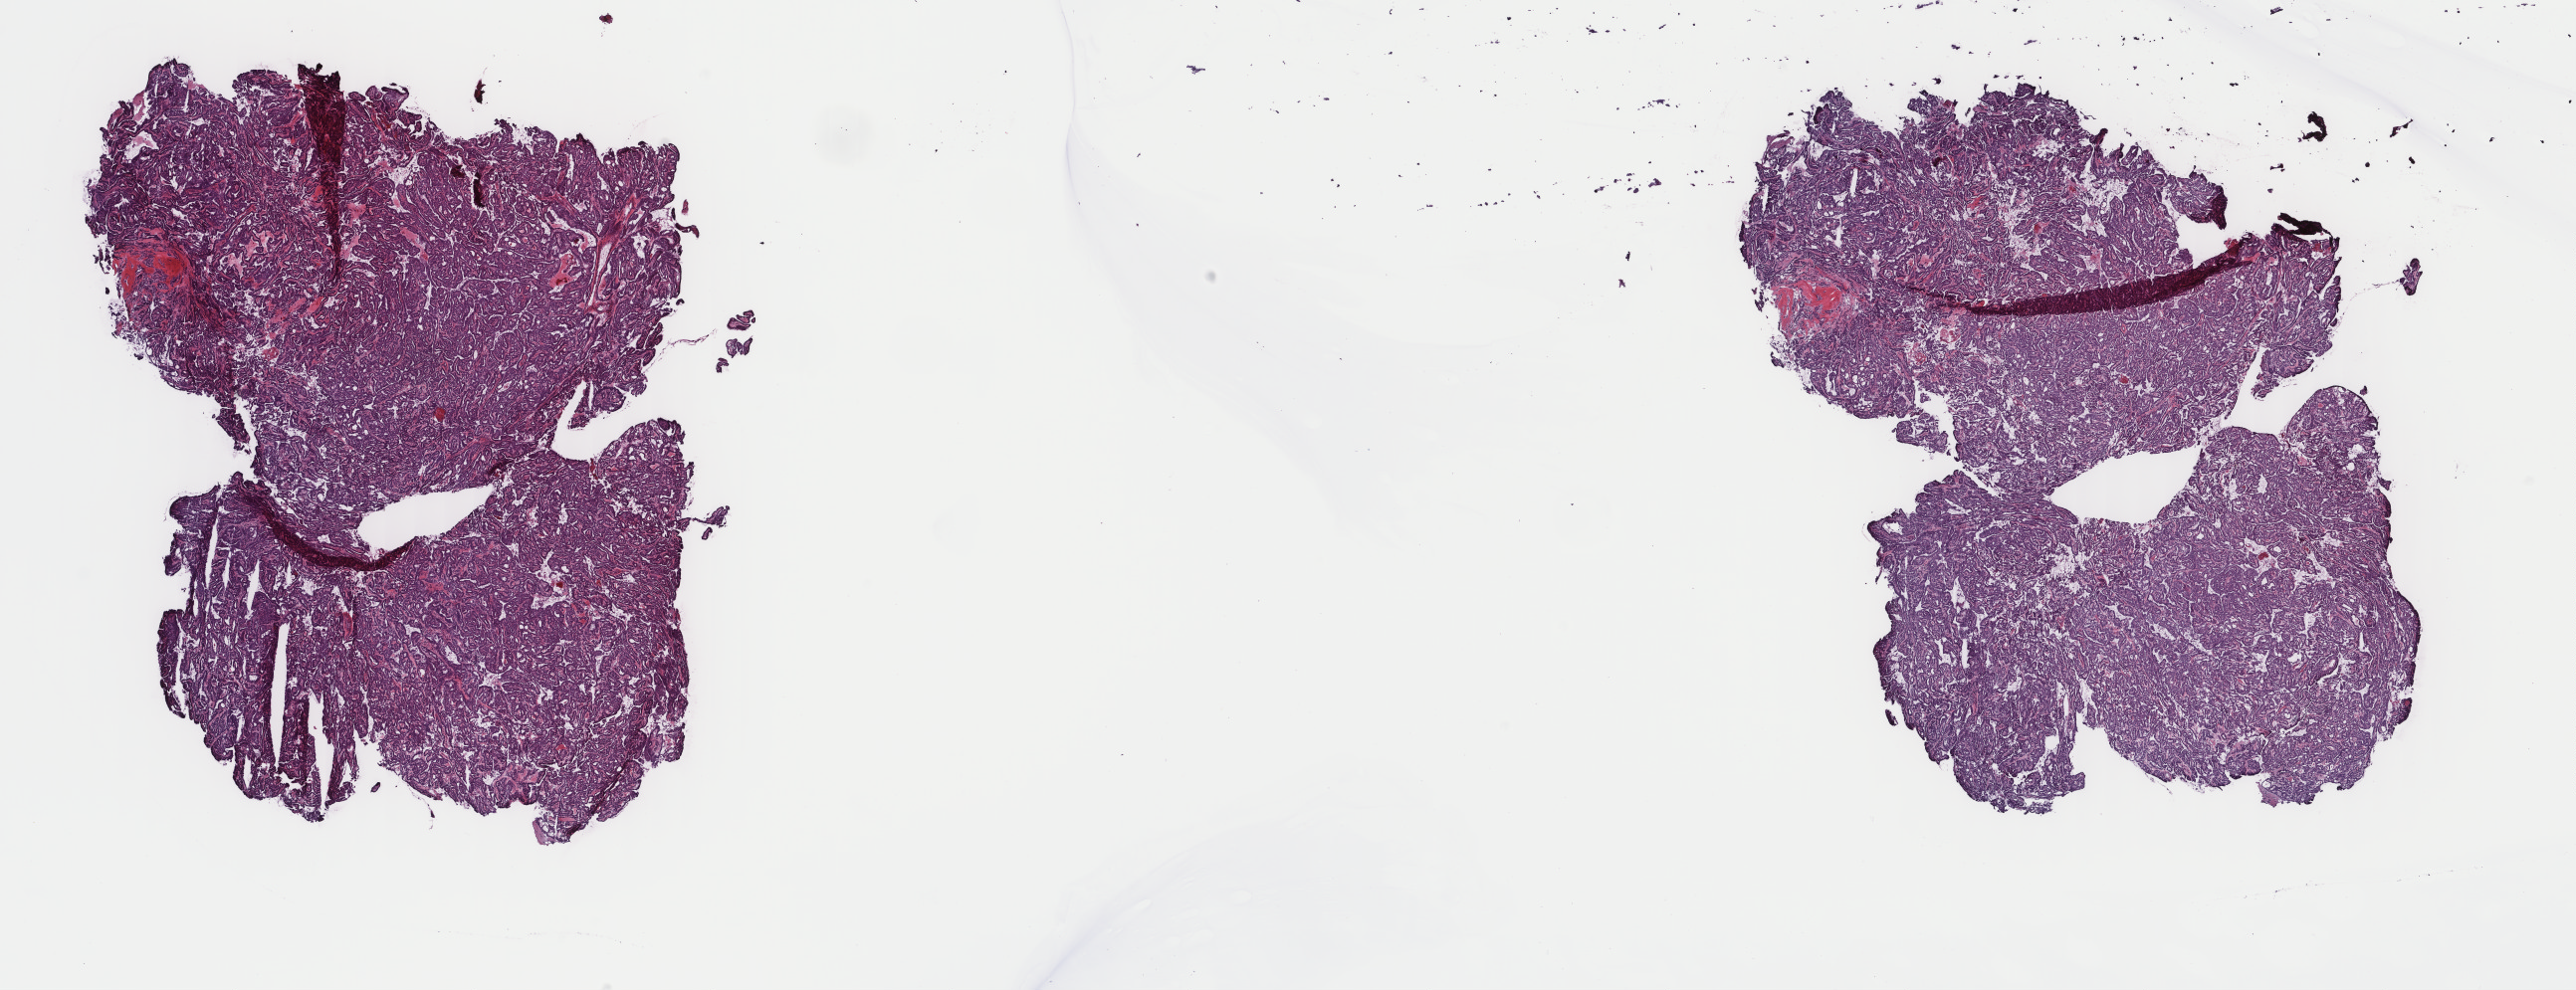
H&E-stained whole-slide image, whole scanned area (about 20.5 x 7.9 mm, acquisition: 40x scan) shown as a low-resolution overview, frozen section, thyroid, primary tumour sample. Patient: female, age at initial diagnosis 29 years. Composition of this section per pathologist review: tumour cells 85%, tumour nuclei 100%, normal cells 0%, stromal cells 15%, necrosis 0%. Infiltration values recorded for this section: lymphocyte infiltration 0%, monocyte infiltration 1%, neutrophil infiltration 0%.
TNM: T3 N0 MX. Diagnosis: Papillary adenocarcinoma, NOS (thyroid gland). AJCC pathologic stage: I (7th edition).